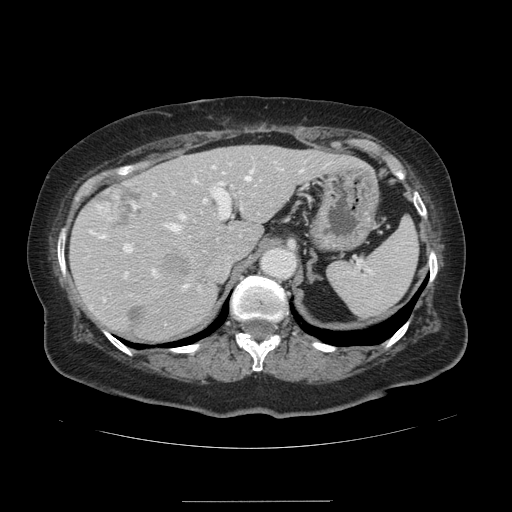
Contrast-enhanced abdominal CT, one axial slice; slice 89 of 141 in the series (ordered by position); 120 kVp; intravenous contrast given; soft-tissue window (W 400 / L 40 HU); 2.5 mm slice thickness; 512 × 512 image matrix, field of view 393 × 393 mm. Female patient, age 74 years. From the clinical record (not read from this slice): diagnosis: colorectal cancer liver metastases, imaged before liver resection; multiple liver metastases: yes; largest metastasis: 7 cm; disease in both lobes: yes.
Annotated regions visible in this slice (expert manual segmentation):
- hepatic veins: bounding box <100,176,250,290> (left, top, right, bottom; pixels)
- liver: <72,146,351,339>
- planned liver remnant (the part of the liver to remain after resection): <72,146,351,339>
- portal vein (with intrahepatic branches): <124,166,301,275>
- liver metastasis: <97,182,142,232>
- liver metastasis: <131,308,141,323>
- liver metastasis: <163,257,189,274>